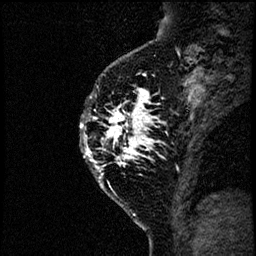
Breast MRI (dynamic contrast-enhanced), one sagittal slice. Position 48 of 60 along the scan axis. Dynamic contrast-enhanced study with each time point stored as its own series, time point 2 of 4 at this slice position (early post-contrast, ordered by acquisition time). 1.5 T. TE 4.2 ms, TR 17.6 ms. 2 mm slice thickness. 256 × 256 image matrix, field of view 200 × 200 mm. Female patient, age 40 years. Case-level facts recorded for this patient, not image findings: setting: breast cancer imaged before/during neoadjuvant chemotherapy; receptor status: HER2-positive.
Outlined on this slice (semi-automatically segmented with operator editing):
- analysis volume of interest (the breast-tissue region the enhancement analysis was run in; not a lesion): bounding box [x1, y1, x2, y2] px = [75, 55, 185, 206]
- tumour enhancement mask (voxels above the 100 % enhancement threshold inside the analysis volume of interest): [79, 72, 160, 179]